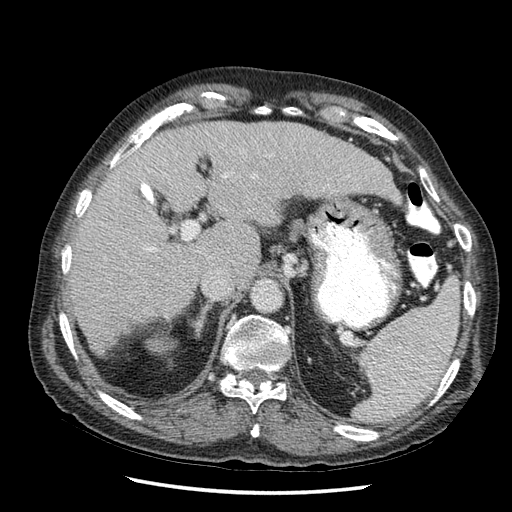
Contrast-enhanced abdominal CT (liver protocol), one axial slice; slice 33 of 67 in the series (ordered by position); reconstruction kernel STANDARD; soft-tissue window (W 400 / L 40 HU); 2.5 mm slice thickness; 512 × 512 image matrix, field of view 360 × 360 mm. Case-level facts recorded for this patient, not image findings: diagnosis: hepatocellular carcinoma (patient treated with transarterial chemoembolisation; whether this scan precedes or follows treatment is not stated here); TNM stage (as recorded): Stage-I; Child-Pugh class: A.
Structures marked on this image (semi-automatic segmentation, software-assisted and operator-edited):
- liver parenchyma outside the tumour (the mass and vessels are separate outlines, so this box may not span the whole liver): bounding box (x1, y1, x2, y2) in pixels: (64, 118, 402, 368)
- liver vessels: (125, 145, 223, 247)